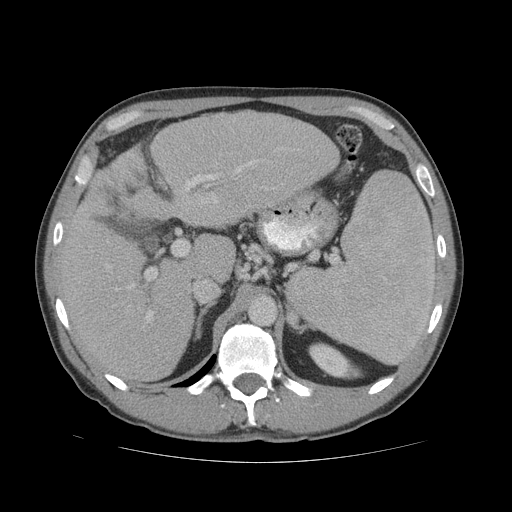
Contrast-enhanced abdominal CT (liver protocol), one axial slice. Slice 40 of 81 in the series (ordered by position). 140 kVp. Soft-tissue window (W 400 / L 40 HU). 2.5 mm slice thickness. 512 × 512 image matrix, field of view 400 × 400 mm. Case-level facts recorded for this patient, not image findings: diagnosis: hepatocellular carcinoma (patient treated with transarterial chemoembolisation; whether this scan precedes or follows treatment is not stated here); TNM stage (as recorded): Stage-IVB; Child-Pugh class: B; tumour differentiation: well differentiated; tumour nodularity: multinodular.
Structures marked on this image (semi-automatic segmentation, software-assisted and operator-edited):
- liver parenchyma outside the tumour (the mass and vessels are separate outlines, so this box may not span the whole liver): box from (x=54, y=110) to (x=340, y=382) px
- liver vessels: (x=107, y=148)–(x=278, y=322)